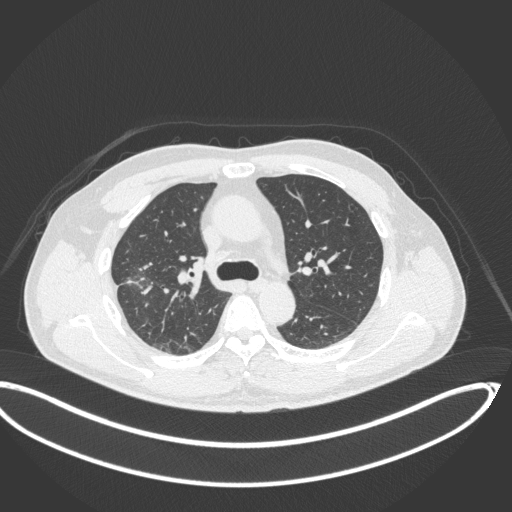
Chest CT, one axial slice. Position 228 of 341 along the scan axis. 120 kVp. Lung window (W 1500 / L -600 HU). 1 mm slice thickness. 512 × 512 image matrix, field of view 439 × 439 mm. Patient: male, 63 years. From the clinical record (not read from this slice): clinical TNM (as recorded): T1c N0 M0; histopathological grade: G2-3.
Structures marked on this image (rectangle marked by the reading radiologist):
- lung tumour (recorded histology: adenocarcinoma): bounding box <123,255,157,301> (left, top, right, bottom; pixels)